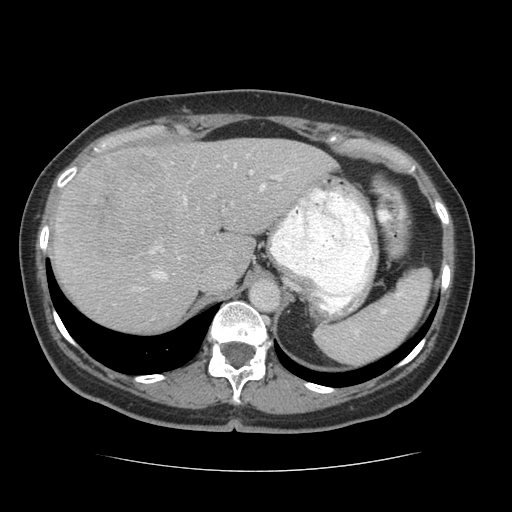
Contrast-enhanced abdominal CT (liver protocol), one axial slice. Position 47 of 75 along the scan axis. Reconstruction kernel STANDARD. Soft-tissue window (W 400 / L 40 HU). 2.5 mm slice thickness. 512 × 512 image matrix. From the clinical record (not read from this slice): diagnosis: hepatocellular carcinoma (patient treated with transarterial chemoembolisation; whether this scan precedes or follows treatment is not stated here); TNM stage (as recorded): Stage-I.
Structures marked on this image (semi-automatically segmented with operator editing):
- liver parenchyma outside the tumour (the mass and vessels are separate outlines, so this box may not span the whole liver): bounding box [x1, y1, x2, y2] px = [52, 138, 336, 332]
- mass: [56, 148, 184, 259]
- liver vessels: [133, 154, 282, 291]